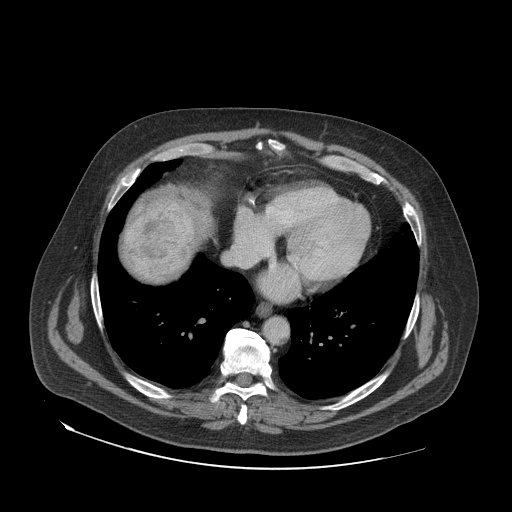
Contrast-enhanced abdominal CT (liver protocol), one axial slice; slice 72 of 79 in the series (ordered by position); reconstruction kernel STANDARD; soft-tissue window (W 400 / L 40 HU); 2.5 mm slice thickness; 512 × 512 image matrix, field of view 480 × 480 mm. From the clinical record (not read from this slice): diagnosis: hepatocellular carcinoma (patient treated with transarterial chemoembolisation; whether this scan precedes or follows treatment is not stated here); TNM stage (as recorded): Stage-IVA; Child-Pugh class: A; tumour differentiation: well differentiated.
Outlined on this slice (semi-automatic segmentation, software-assisted and operator-edited):
- liver parenchyma outside the tumour (the mass and vessels are separate outlines, so this box may not span the whole liver): bounding box (x1, y1, x2, y2) in pixels: (124, 196, 210, 276)
- mass: (123, 197, 195, 282)